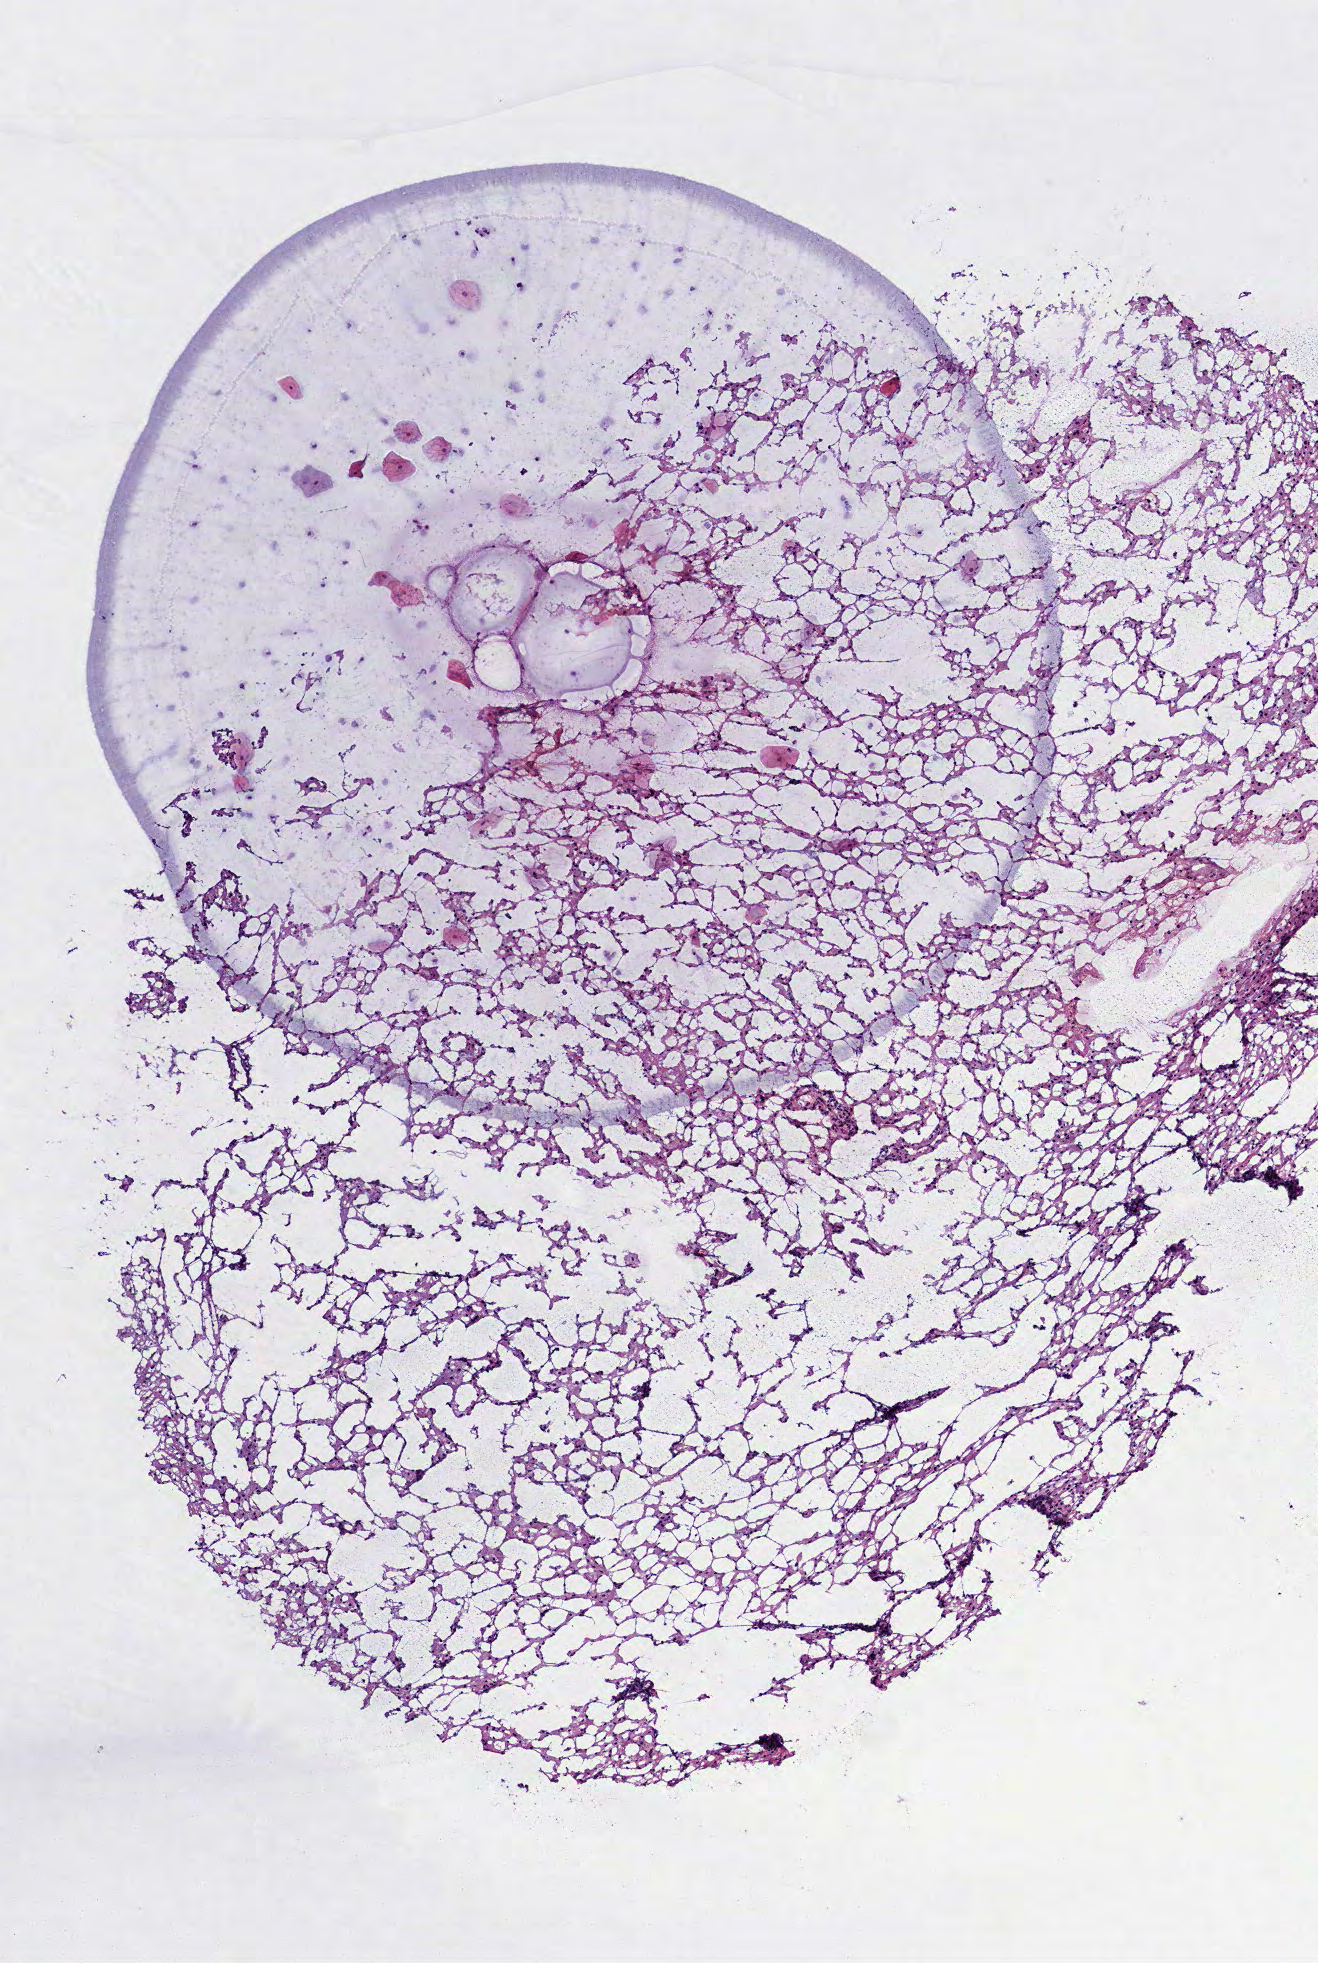
H&E-stained whole-slide image, whole scanned area (about 2.7 x 4.0 mm, acquisition: 40x scan) shown as a low-resolution overview, frozen section from the top of the tissue portion, primary tumour sample from the brain. Male, age 28 years at initial diagnosis. Histologic grade: G2 (moderately differentiated). Composition of this section per pathologist review: tumour cells 100%, tumour nuclei 60%, normal cells 0%, stromal cells 0%, necrosis 0%.
* pathologic diagnosis: Mixed glioma
* laterality: right